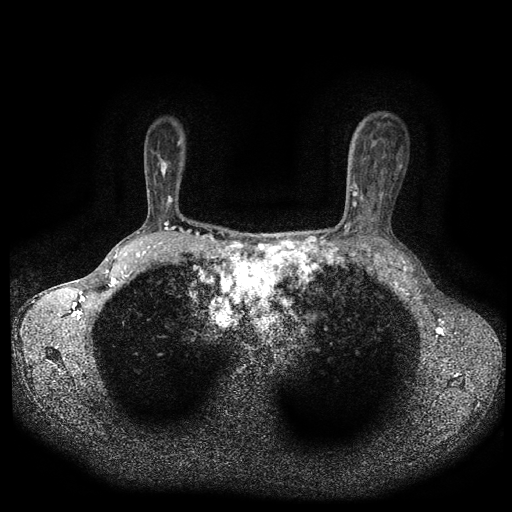
Breast MRI (dynamic contrast-enhanced, multi-phase), one axial slice. Position 73 of 116 along the scan axis. Dynamic contrast-enhanced series, time point 2 of 5 at this slice position (early post-contrast). 1.5 T. TE 2.7 ms, TR 5.4 ms. 512 × 512 image matrix, field of view 330 × 330 mm. Patient: female, 49 years.
Annotated regions visible in this slice (semi-automatically segmented with operator editing):
- breast lesion (labelled benign in the annotation): box from (x=156, y=148) to (x=169, y=181) px